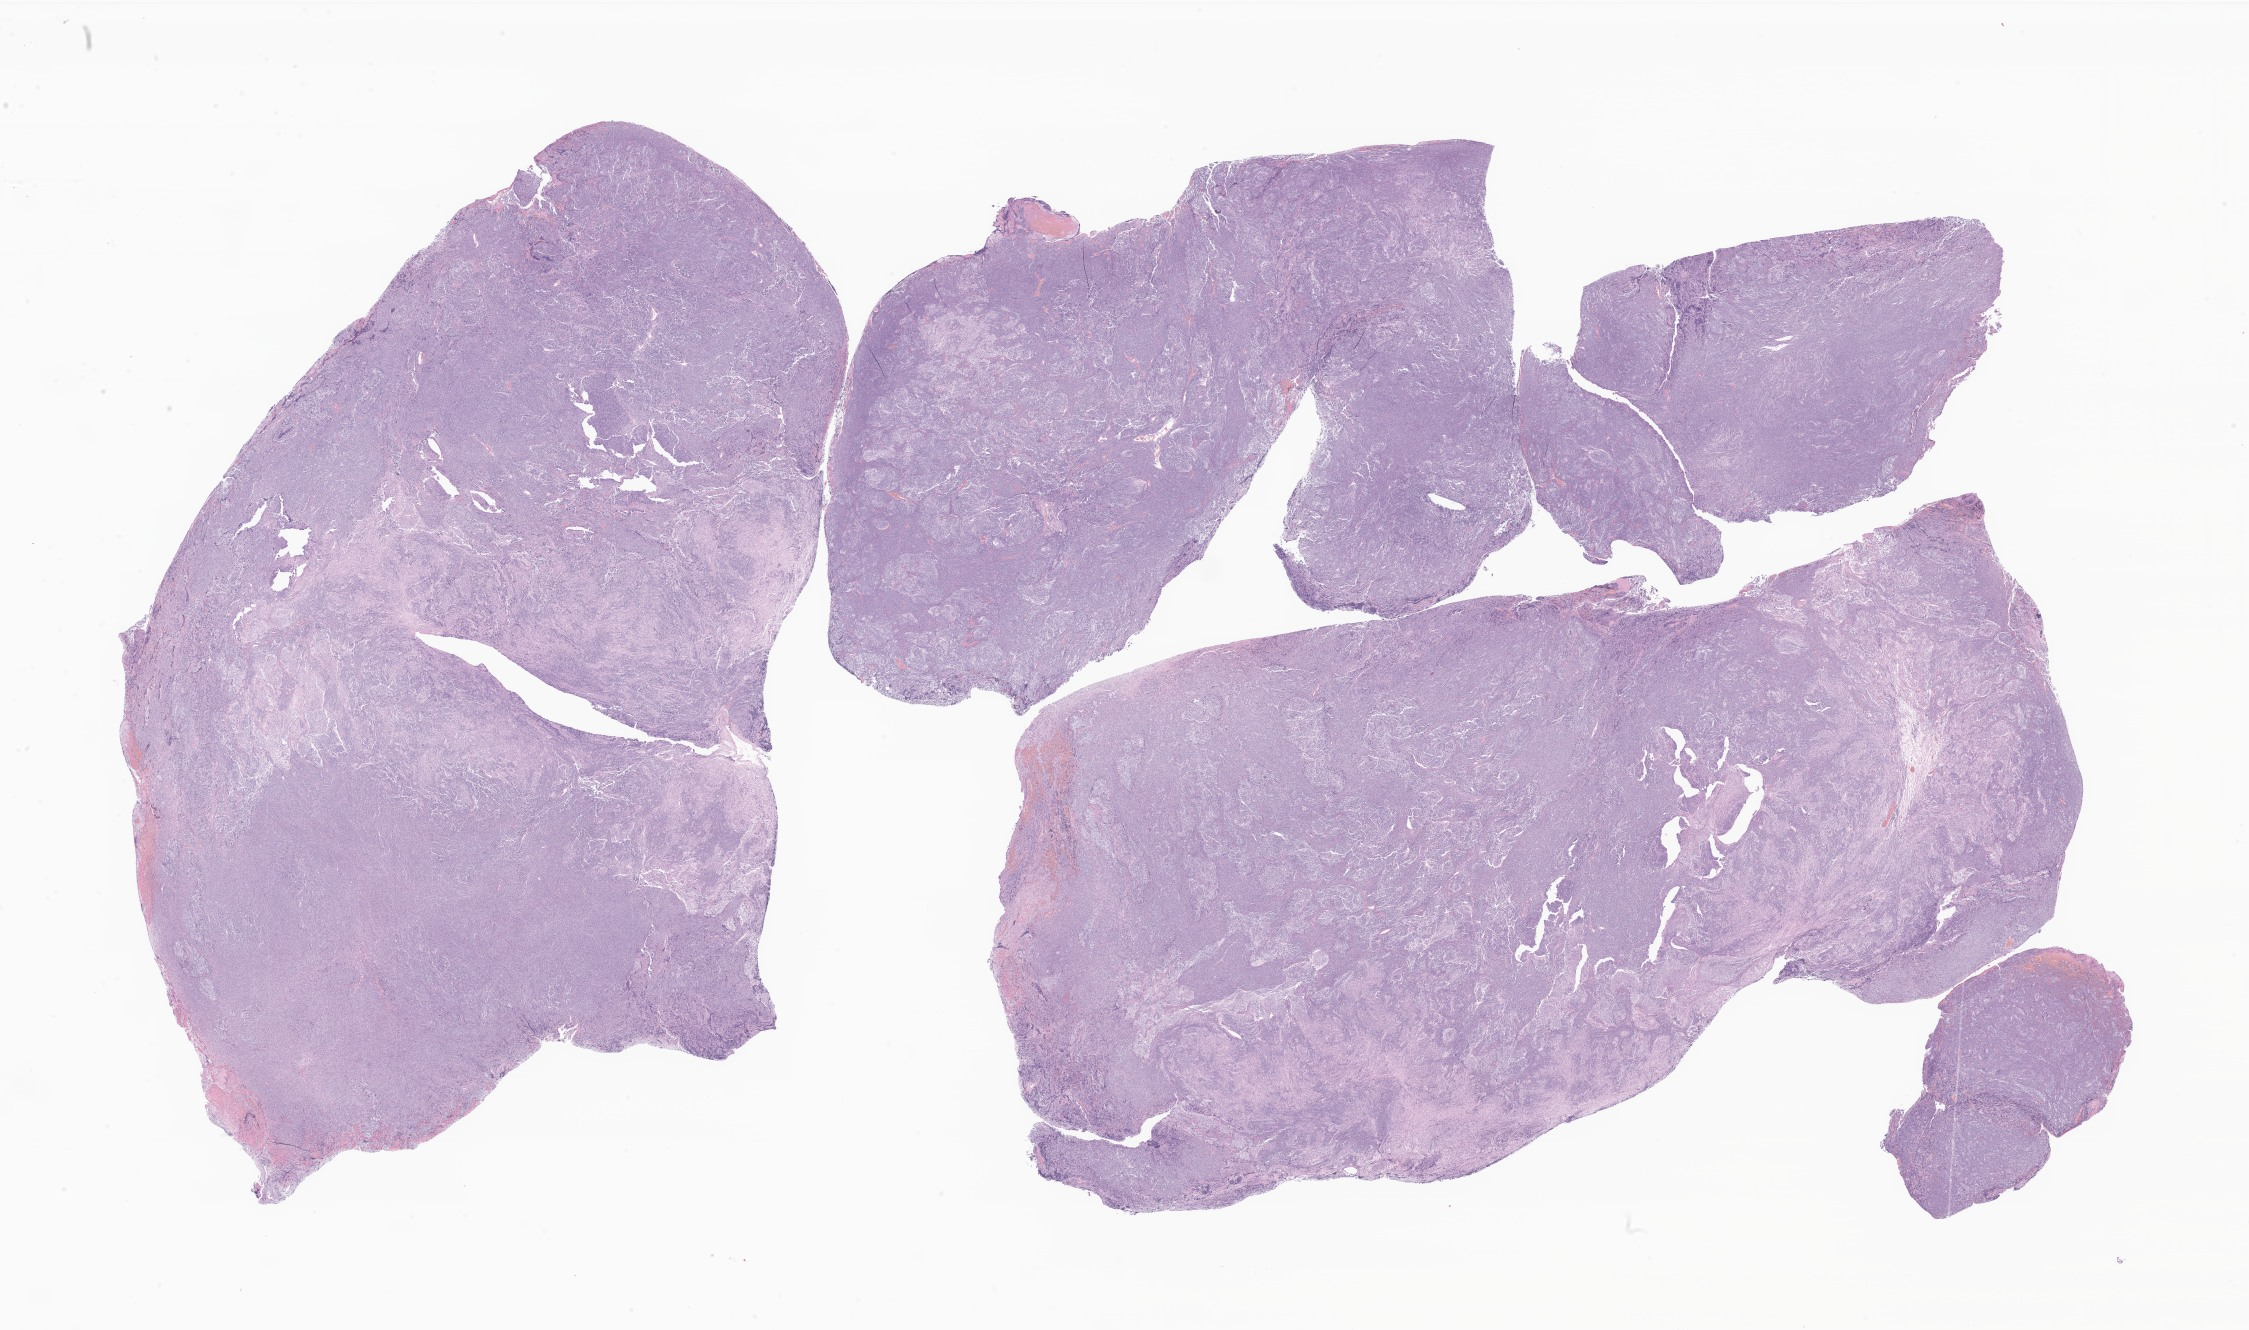
Digitized H&E-stained section of tumor tissue from the cerebellum, whole scanned area (about 37.9 x 22.4 mm) shown as a low-resolution overview, formalin-fixed paraffin-embedded section. Patient: female, age 690 days (about 1.9 years).
• diagnosis: Medulloblastoma, NOS